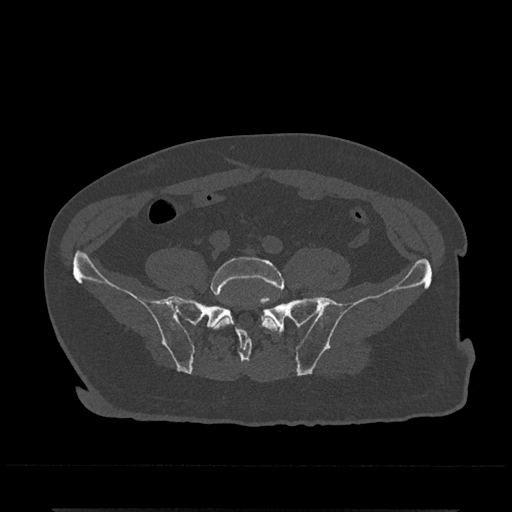
CT including the spine, one axial slice. Slice 54 of 797 in the series (ordered by position). Bone window (W 1800 / L 400 HU). 0.5 mm slice thickness. 512 × 512 image matrix, field of view 393 × 393 mm. Male patient, age 67 years. Case-level facts recorded for this patient, not image findings: primary cancer: prostate.
Structures marked on this image (semi-automatic segmentation, software-assisted and operator-edited):
- L5 vertebra: bounding box <210,256,284,332> (left, top, right, bottom; pixels)